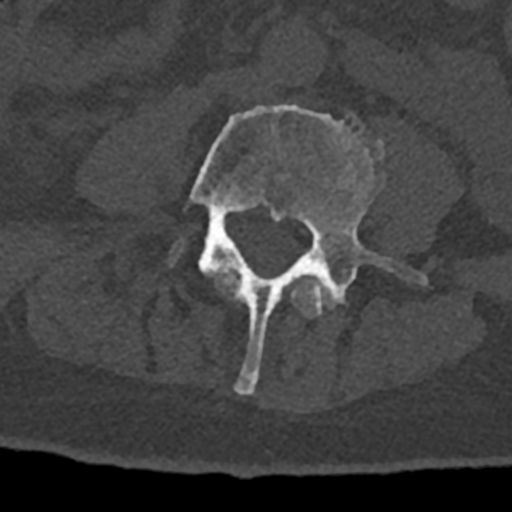
CT including the spine, one axial slice. Position 264 of 797 along the scan axis. 120 kVp. Bone window (W 1800 / L 400 HU). 0.5 mm slice thickness. 512 × 512 image matrix, field of view 160 × 160 mm. Patient: male, 74 years. Case-level facts recorded for this patient, not image findings: primary cancer: renal.
Annotated regions visible in this slice (semi-automatically segmented with operator editing):
- L3 vertebra: box from (x=209, y=268) to (x=333, y=317) px
- L4 vertebra: (x=185, y=105)–(x=427, y=394)
- L5 vertebra: (x=172, y=247)–(x=182, y=261)